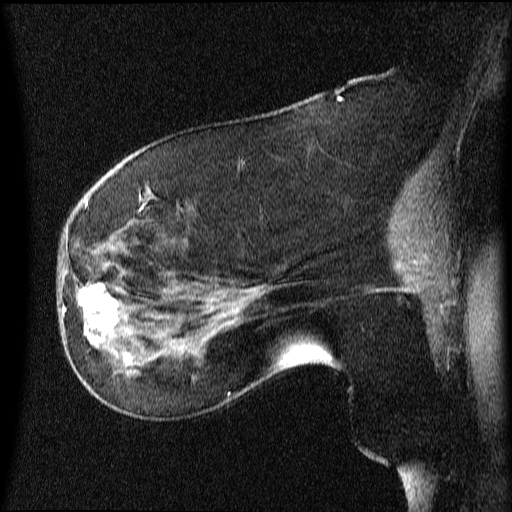
Breast MRI (dynamic contrast-enhanced), one sagittal slice. Slice 27 of 64 in the series (ordered by position). Dynamic contrast-enhanced series, image 2 of 4 at this slice position (ordered by acquisition). 1.5 T. TE 4.2 ms, TR 9 ms. 2 mm slice thickness. 512 × 512 image matrix. Patient: female, 63 years.
Annotated regions visible in this slice (semi-automatic segmentation, software-assisted and operator-edited):
- analysis volume of interest (the breast-tissue region the enhancement analysis was run in; not a lesion): bounding box <66,272,131,353> (left, top, right, bottom; pixels)
- tumour enhancement mask (voxels above the 70 % enhancement threshold inside the analysis volume of interest): <82,284,118,347>